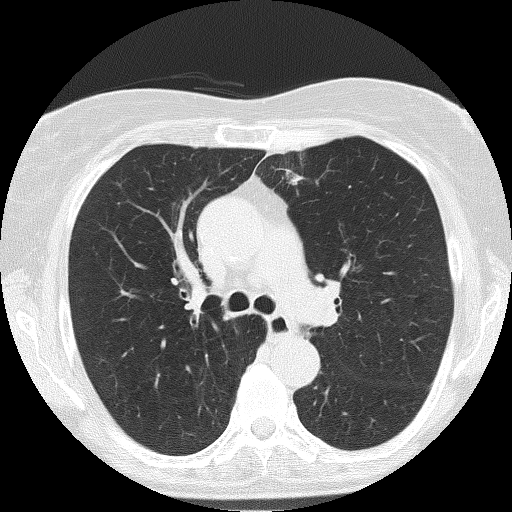
Low-dose screening chest CT, one axial slice; position 113 of 166 along the scan axis; lung window (W 1500 / L -600 HU); 2 mm slice thickness; 512 × 512 image matrix, field of view 303 × 303 mm.
Outlined on this slice (outlined manually by an expert reader):
- lesion 2 (nodule, upper lobe of left lung): bounding box <292,178,296,182> (left, top, right, bottom; pixels)